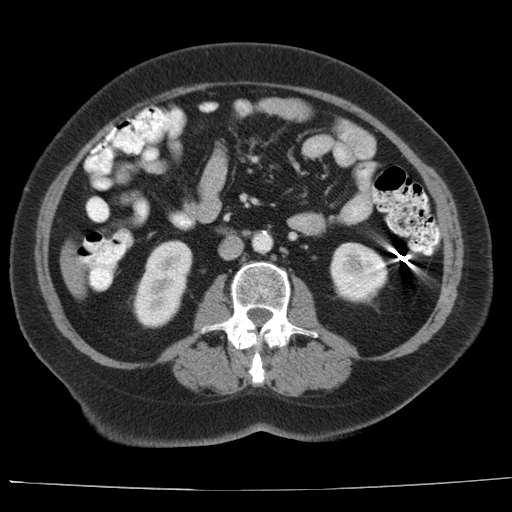
Contrast-enhanced abdominal CT, one axial slice; position 2 of 44 along the scan axis; intravenous contrast given; soft-tissue window (W 400 / L 40 HU); 5 mm slice thickness; 512 × 512 image matrix. Female patient. Case-level facts recorded for this patient, not image findings: diagnosis: colorectal cancer liver metastases, imaged before liver resection; multiple liver metastases: yes; largest metastasis: 1.8 cm; disease in both lobes: no.
Annotated regions visible in this slice (outlined manually by an expert reader):
- liver: bounding box <61,244,86,297> (left, top, right, bottom; pixels)